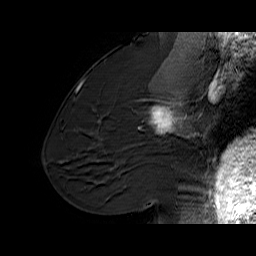
Breast MRI (dynamic contrast-enhanced), one sagittal slice. Position 33 of 60 along the scan axis. Dynamic contrast-enhanced series, time point 2 of 6 at this slice position (early post-contrast). 1.5 T. TE 6.1 ms, TR 32.9 ms. 256 × 256 image matrix. Female patient. From the clinical record (not read from this slice): setting: breast cancer imaged before/during neoadjuvant chemotherapy; receptor status: HER2-positive.
Structures marked on this image (semi-automatic segmentation, software-assisted and operator-edited):
- analysis volume of interest (the breast-tissue region the enhancement analysis was run in; not a lesion): bounding box <127,95,194,165> (left, top, right, bottom; pixels)
- tumour enhancement mask (voxels above the 100 % enhancement threshold inside the analysis volume of interest): <139,101,191,138>